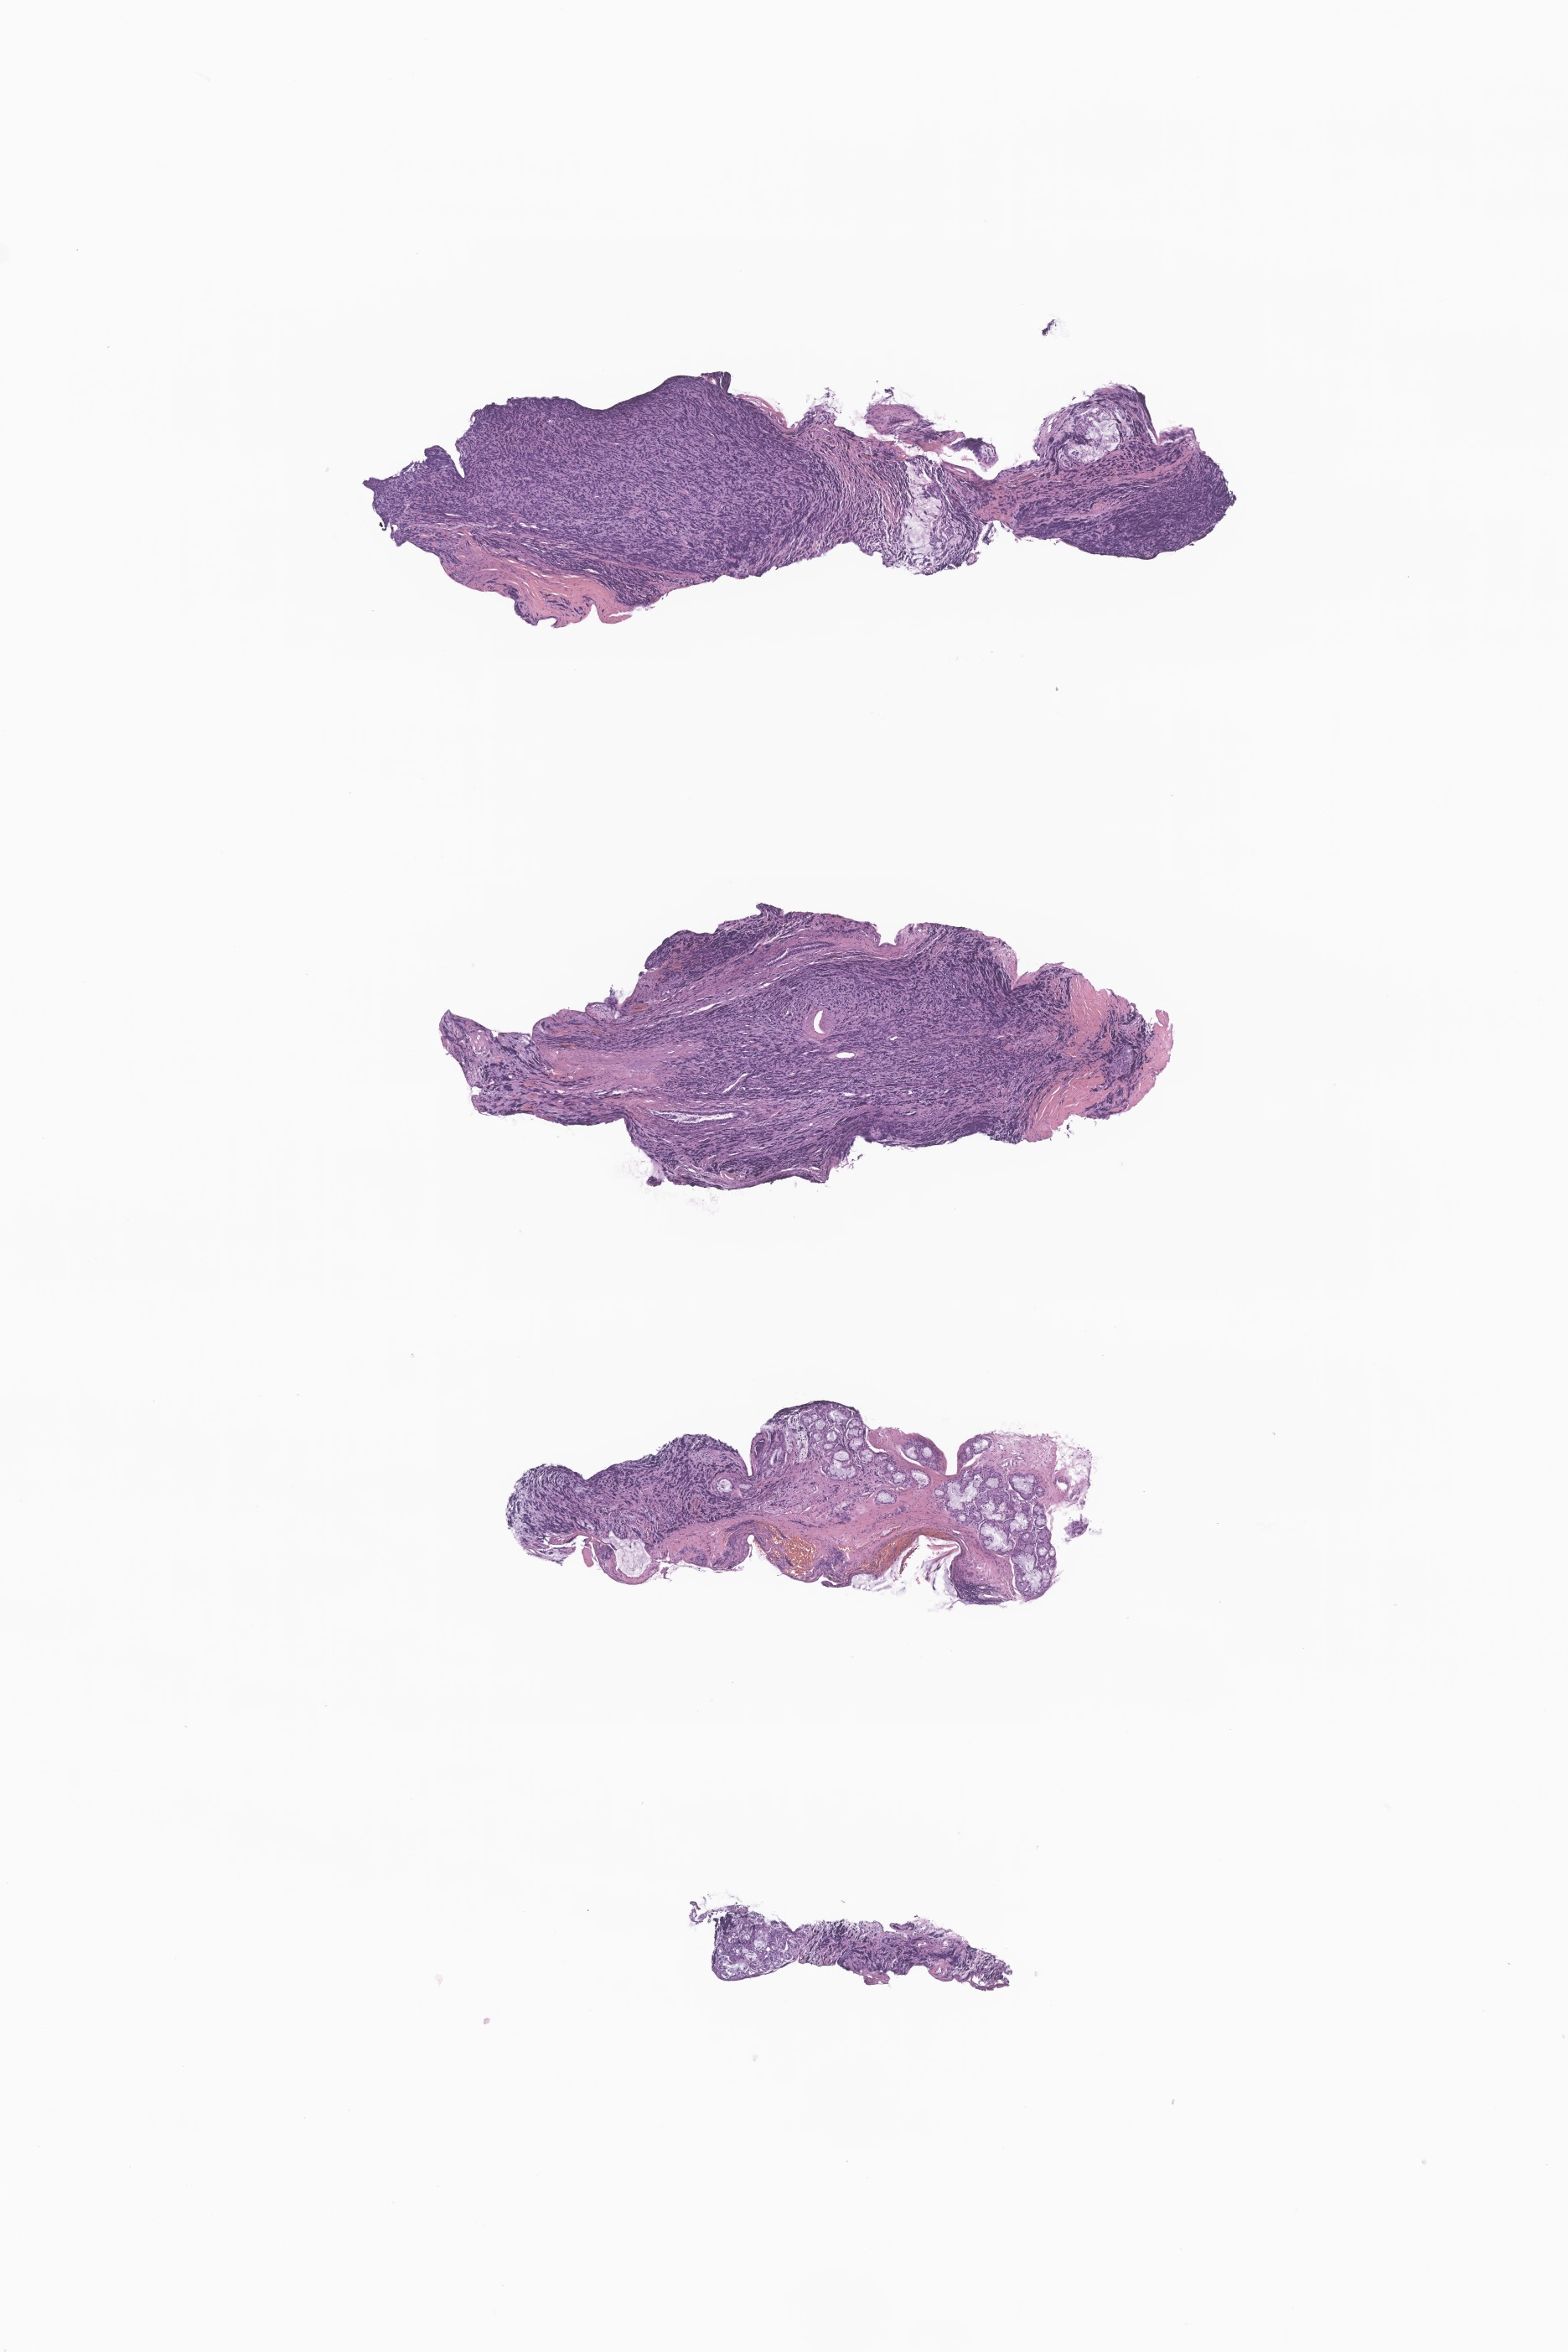
Whole-slide image, hematoxylin and eosin (H&E) stain of tumor tissue from the nasopharynx — a low-resolution overview of the entire scanned area, about 7.9 x 11.8 mm, formalin-fixed, paraffin-embedded (FFPE) tissue. Patient: male, age 66 months (5 years 6 months).
Diagnosis: Rhabdomyosarcoma, NOS.